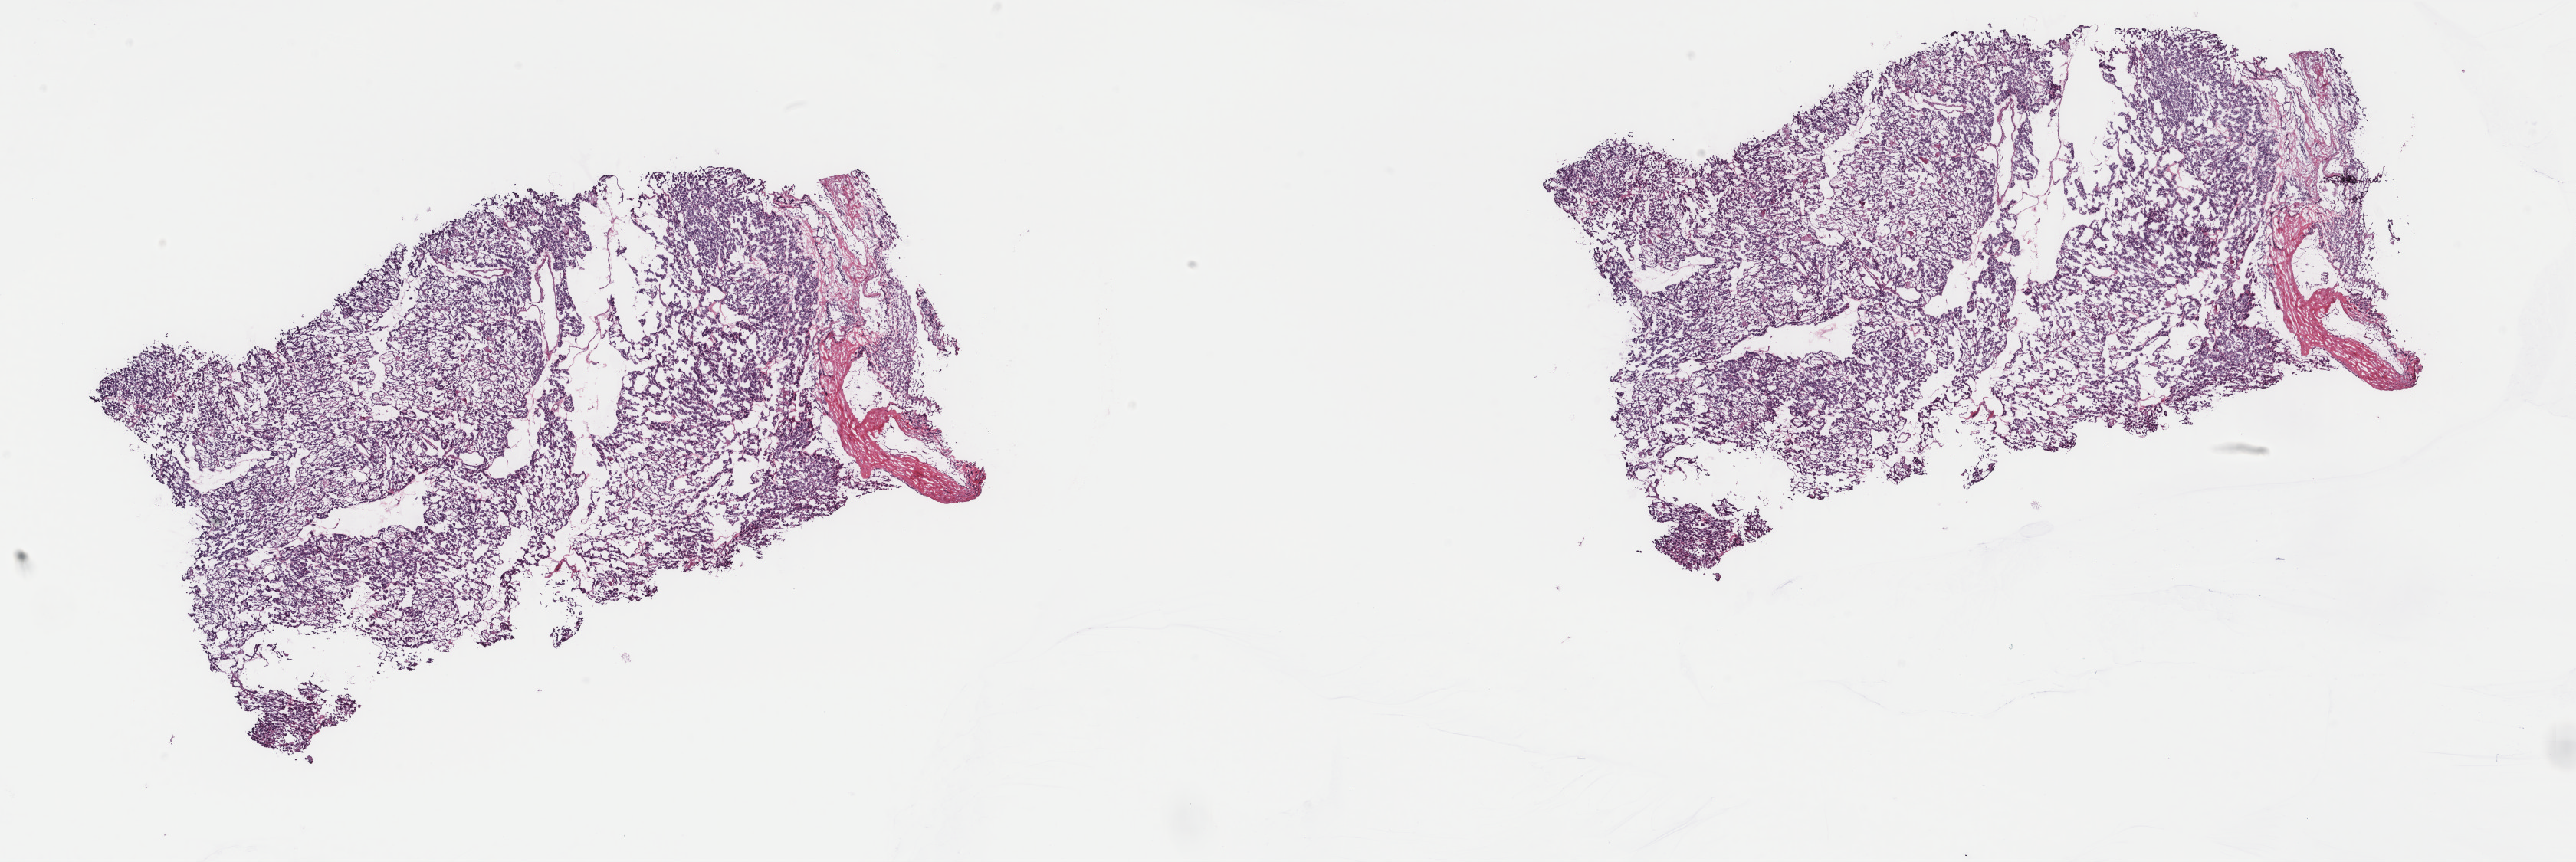
H&E whole-slide image — shown as a low-resolution overview of the whole scanned area (about 26.7 x 8.9 mm, from a 40x scan). Frozen section from the top of the tissue portion. Thyroid, primary tumour sample. Female, age 33 years at initial diagnosis.
Diagnosis: Papillary carcinoma, follicular variant.